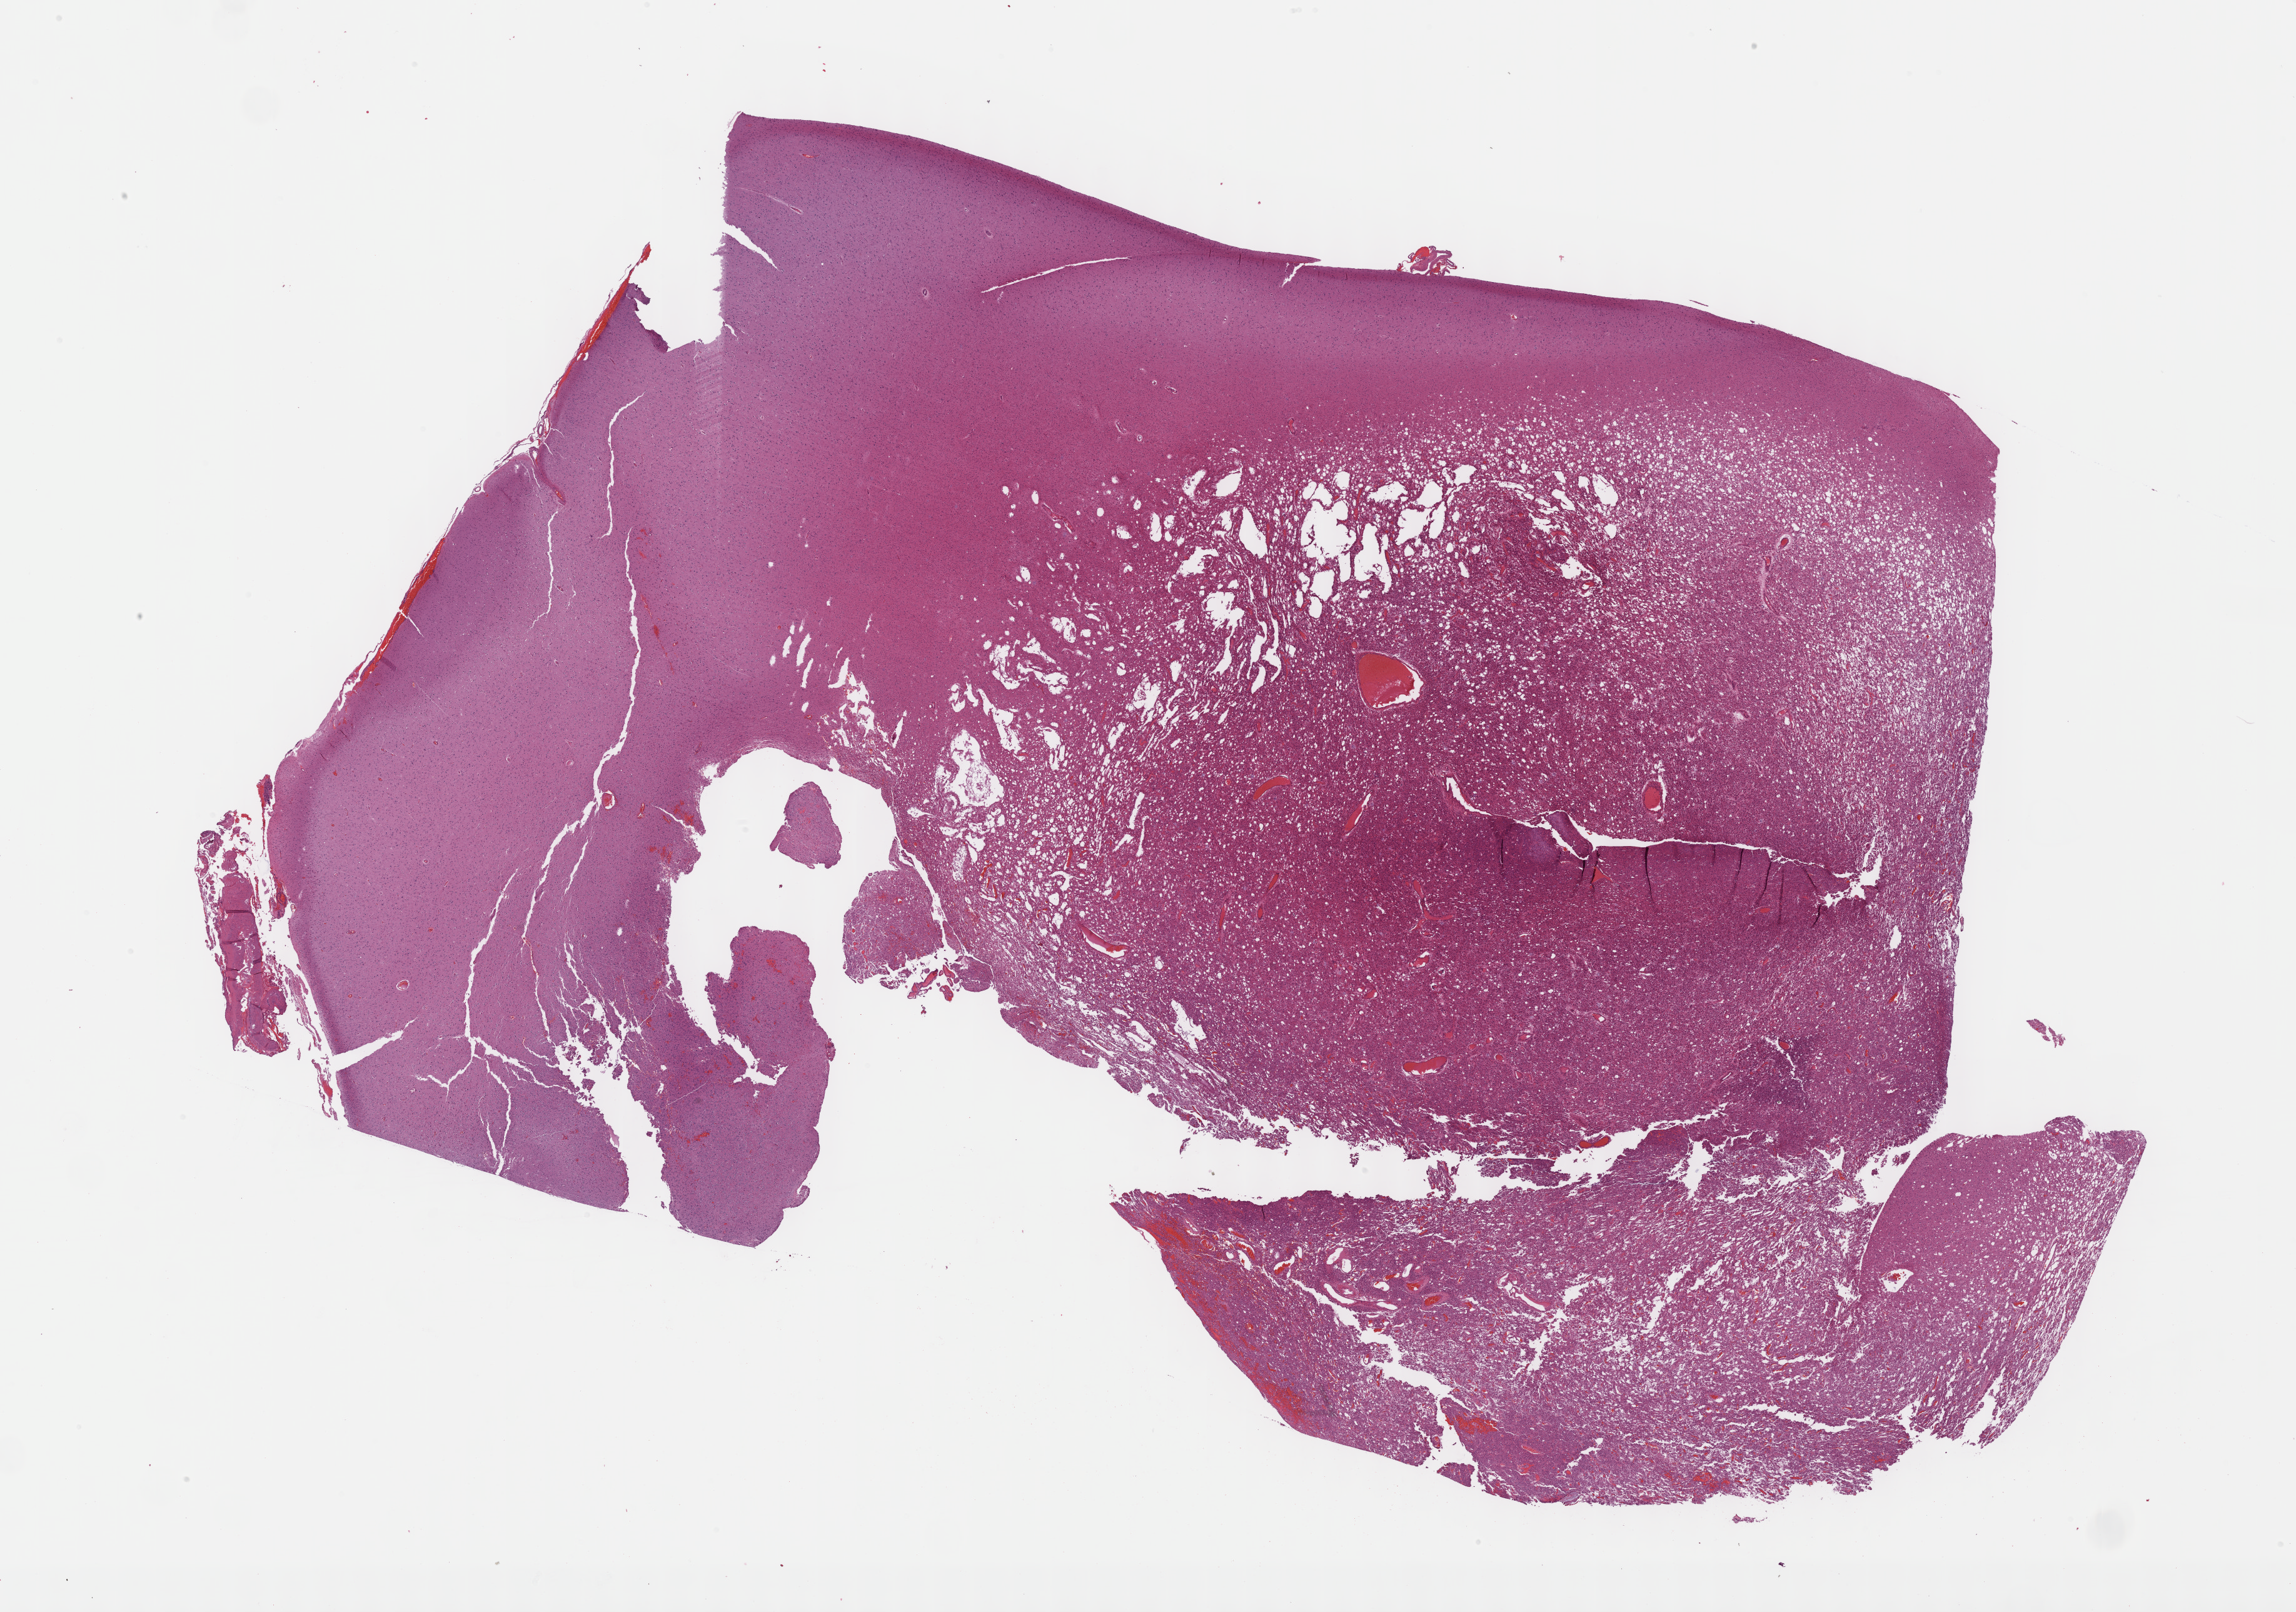
Digitized H&E-stained tissue section (whole slide) — shown as a low-resolution overview of the whole scanned area (about 29.7 x 20.9 mm, acquisition: 40x scan). FFPE section. Primary tumour sample from the brain. Male, age 61 years at initial diagnosis. Histologic grade: G2 (moderately differentiated).
Diagnosis: Mixed glioma (cerebrum). Laterality: right.